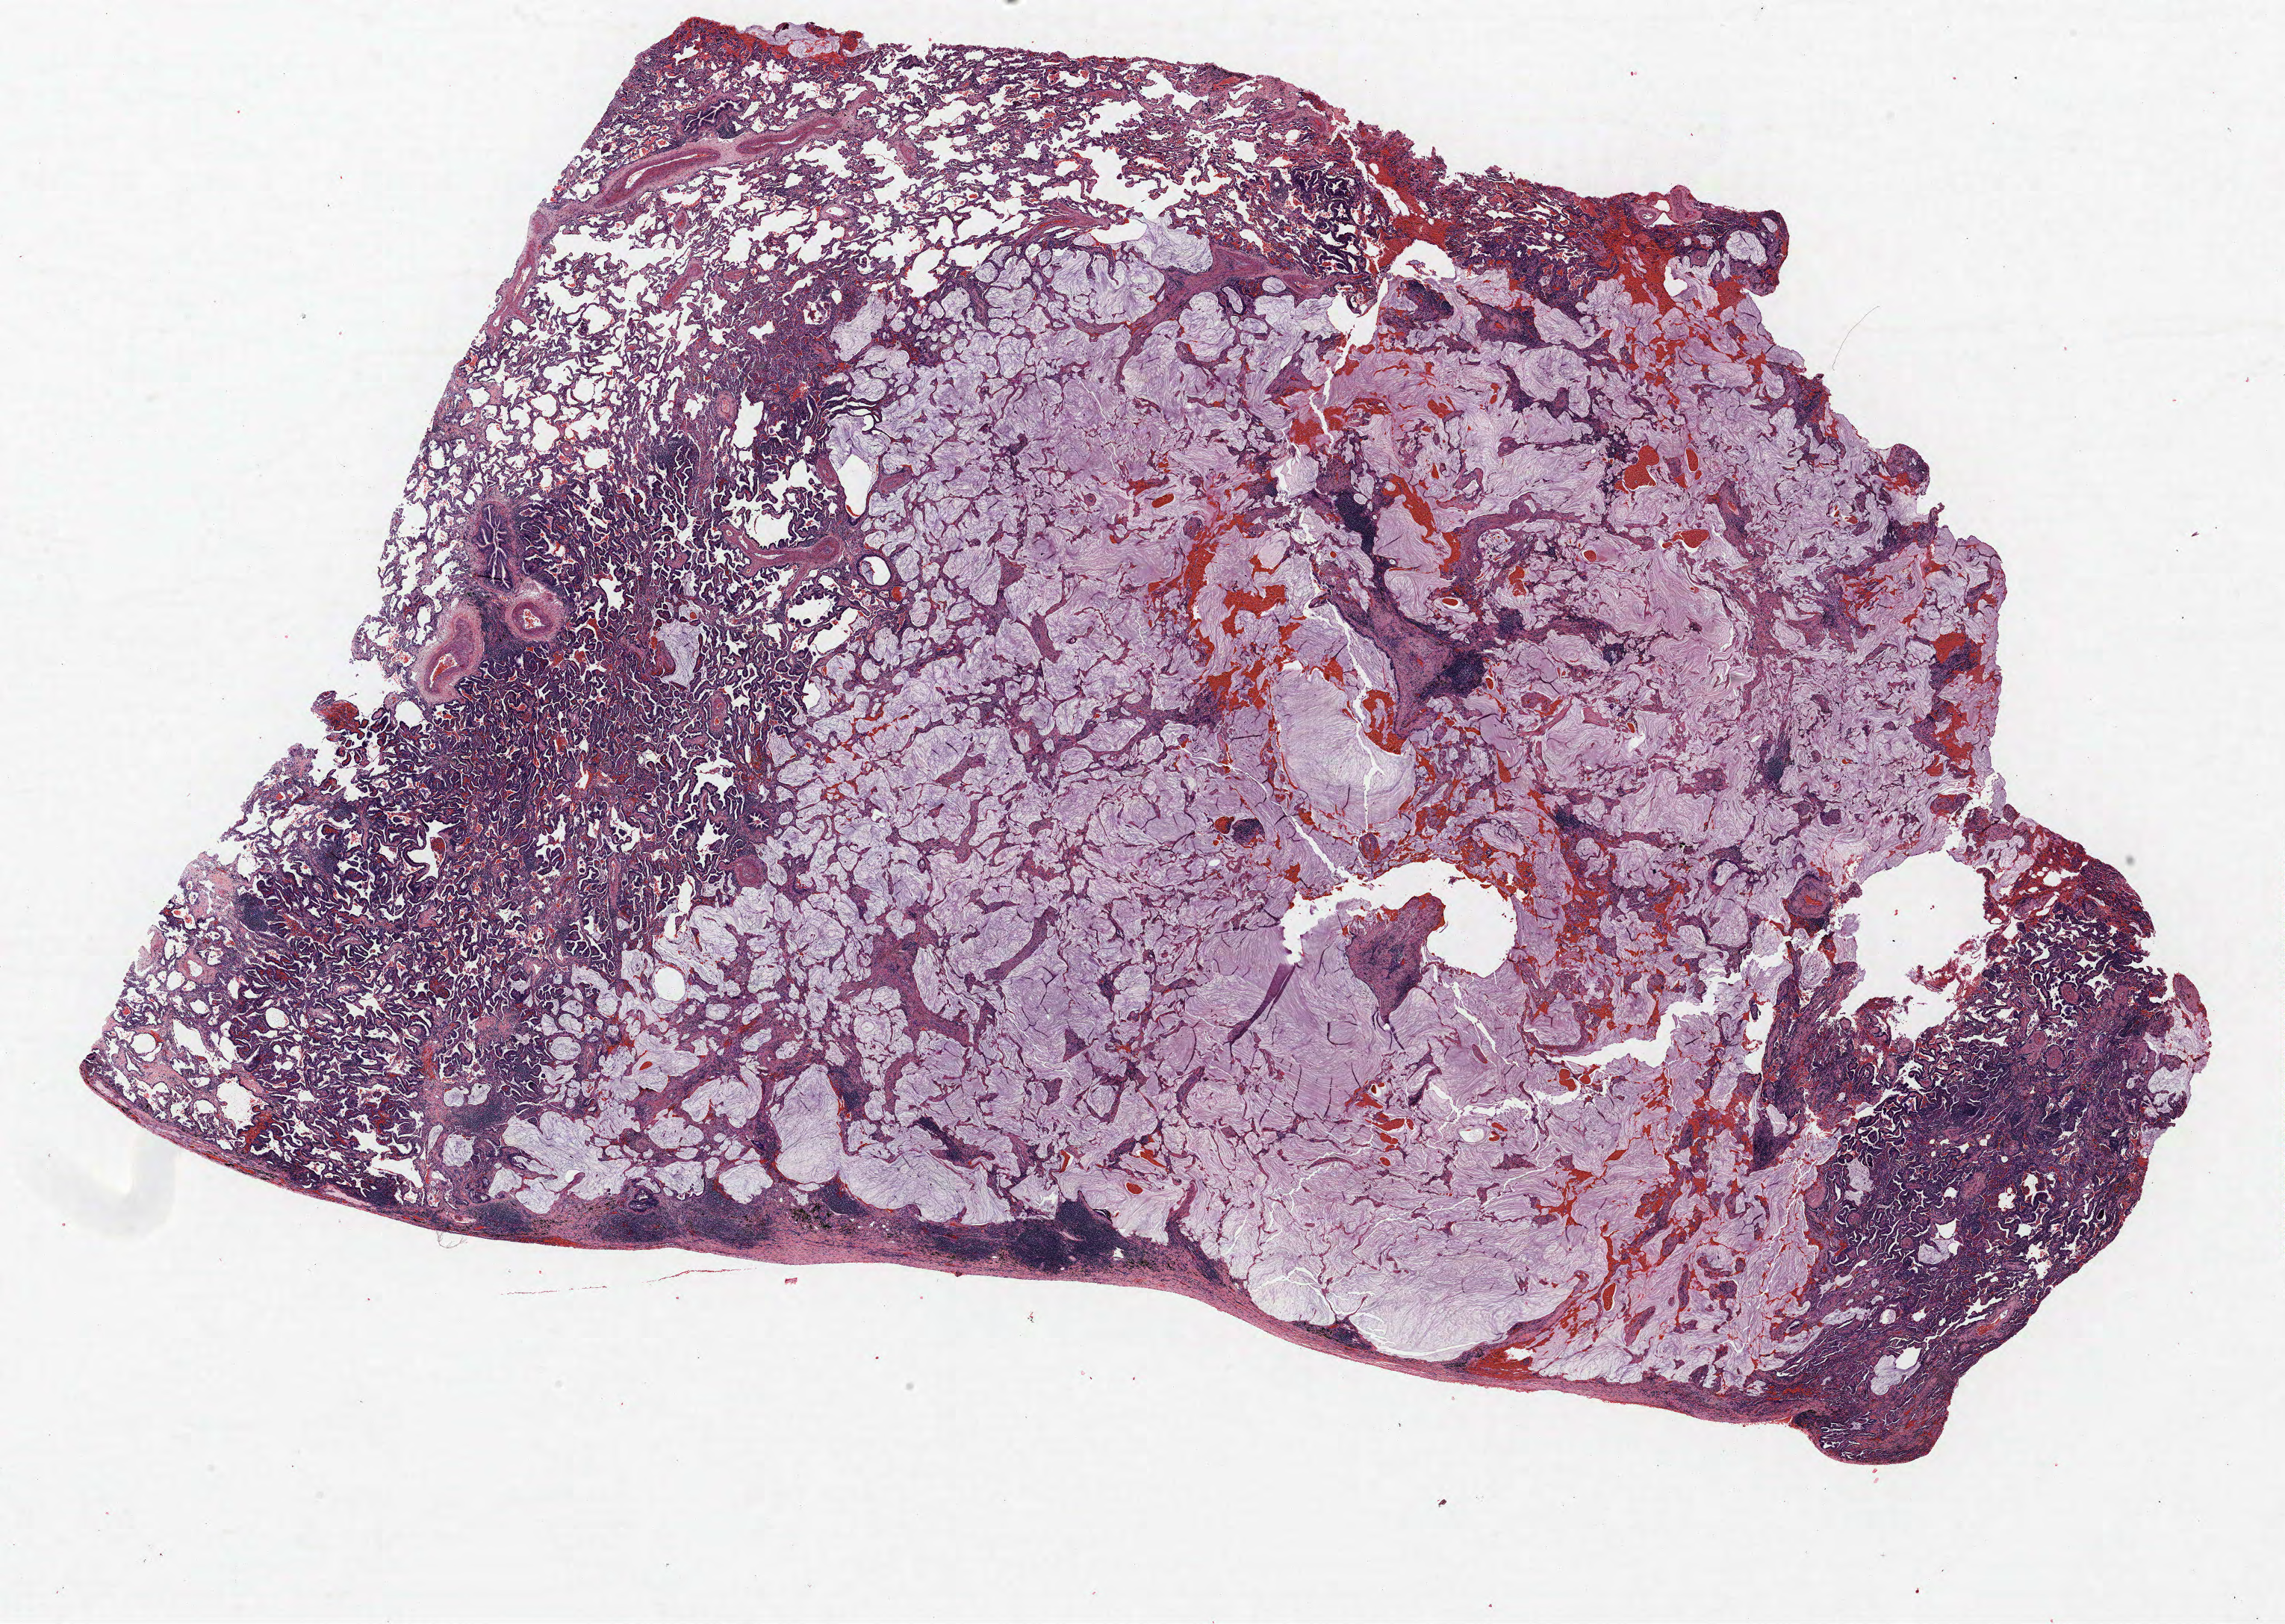
Whole-slide histology image, Hematoxylin and eosin (H&E) stained, a low-resolution overview of the entire scanned area, about 24.5 x 17.4 mm. Formalin-fixed paraffin-embedded (FFPE) section. Lung. Male, age 67 at enrolment. Current smoker at enrolment. Grade: well differentiated (G1).
Tumour size (pathology): 65 mm. ICD-O-3 topography: lower lobe of lung (C34.3). Participant's lung-cancer diagnosis: Bronchiolo-alveolar carcinoma, non-mucinous (ICD-O-3 8252/3). Primary tumour location (clinical record): right lower lobe. Stage (AJCC 6th edition): IB.